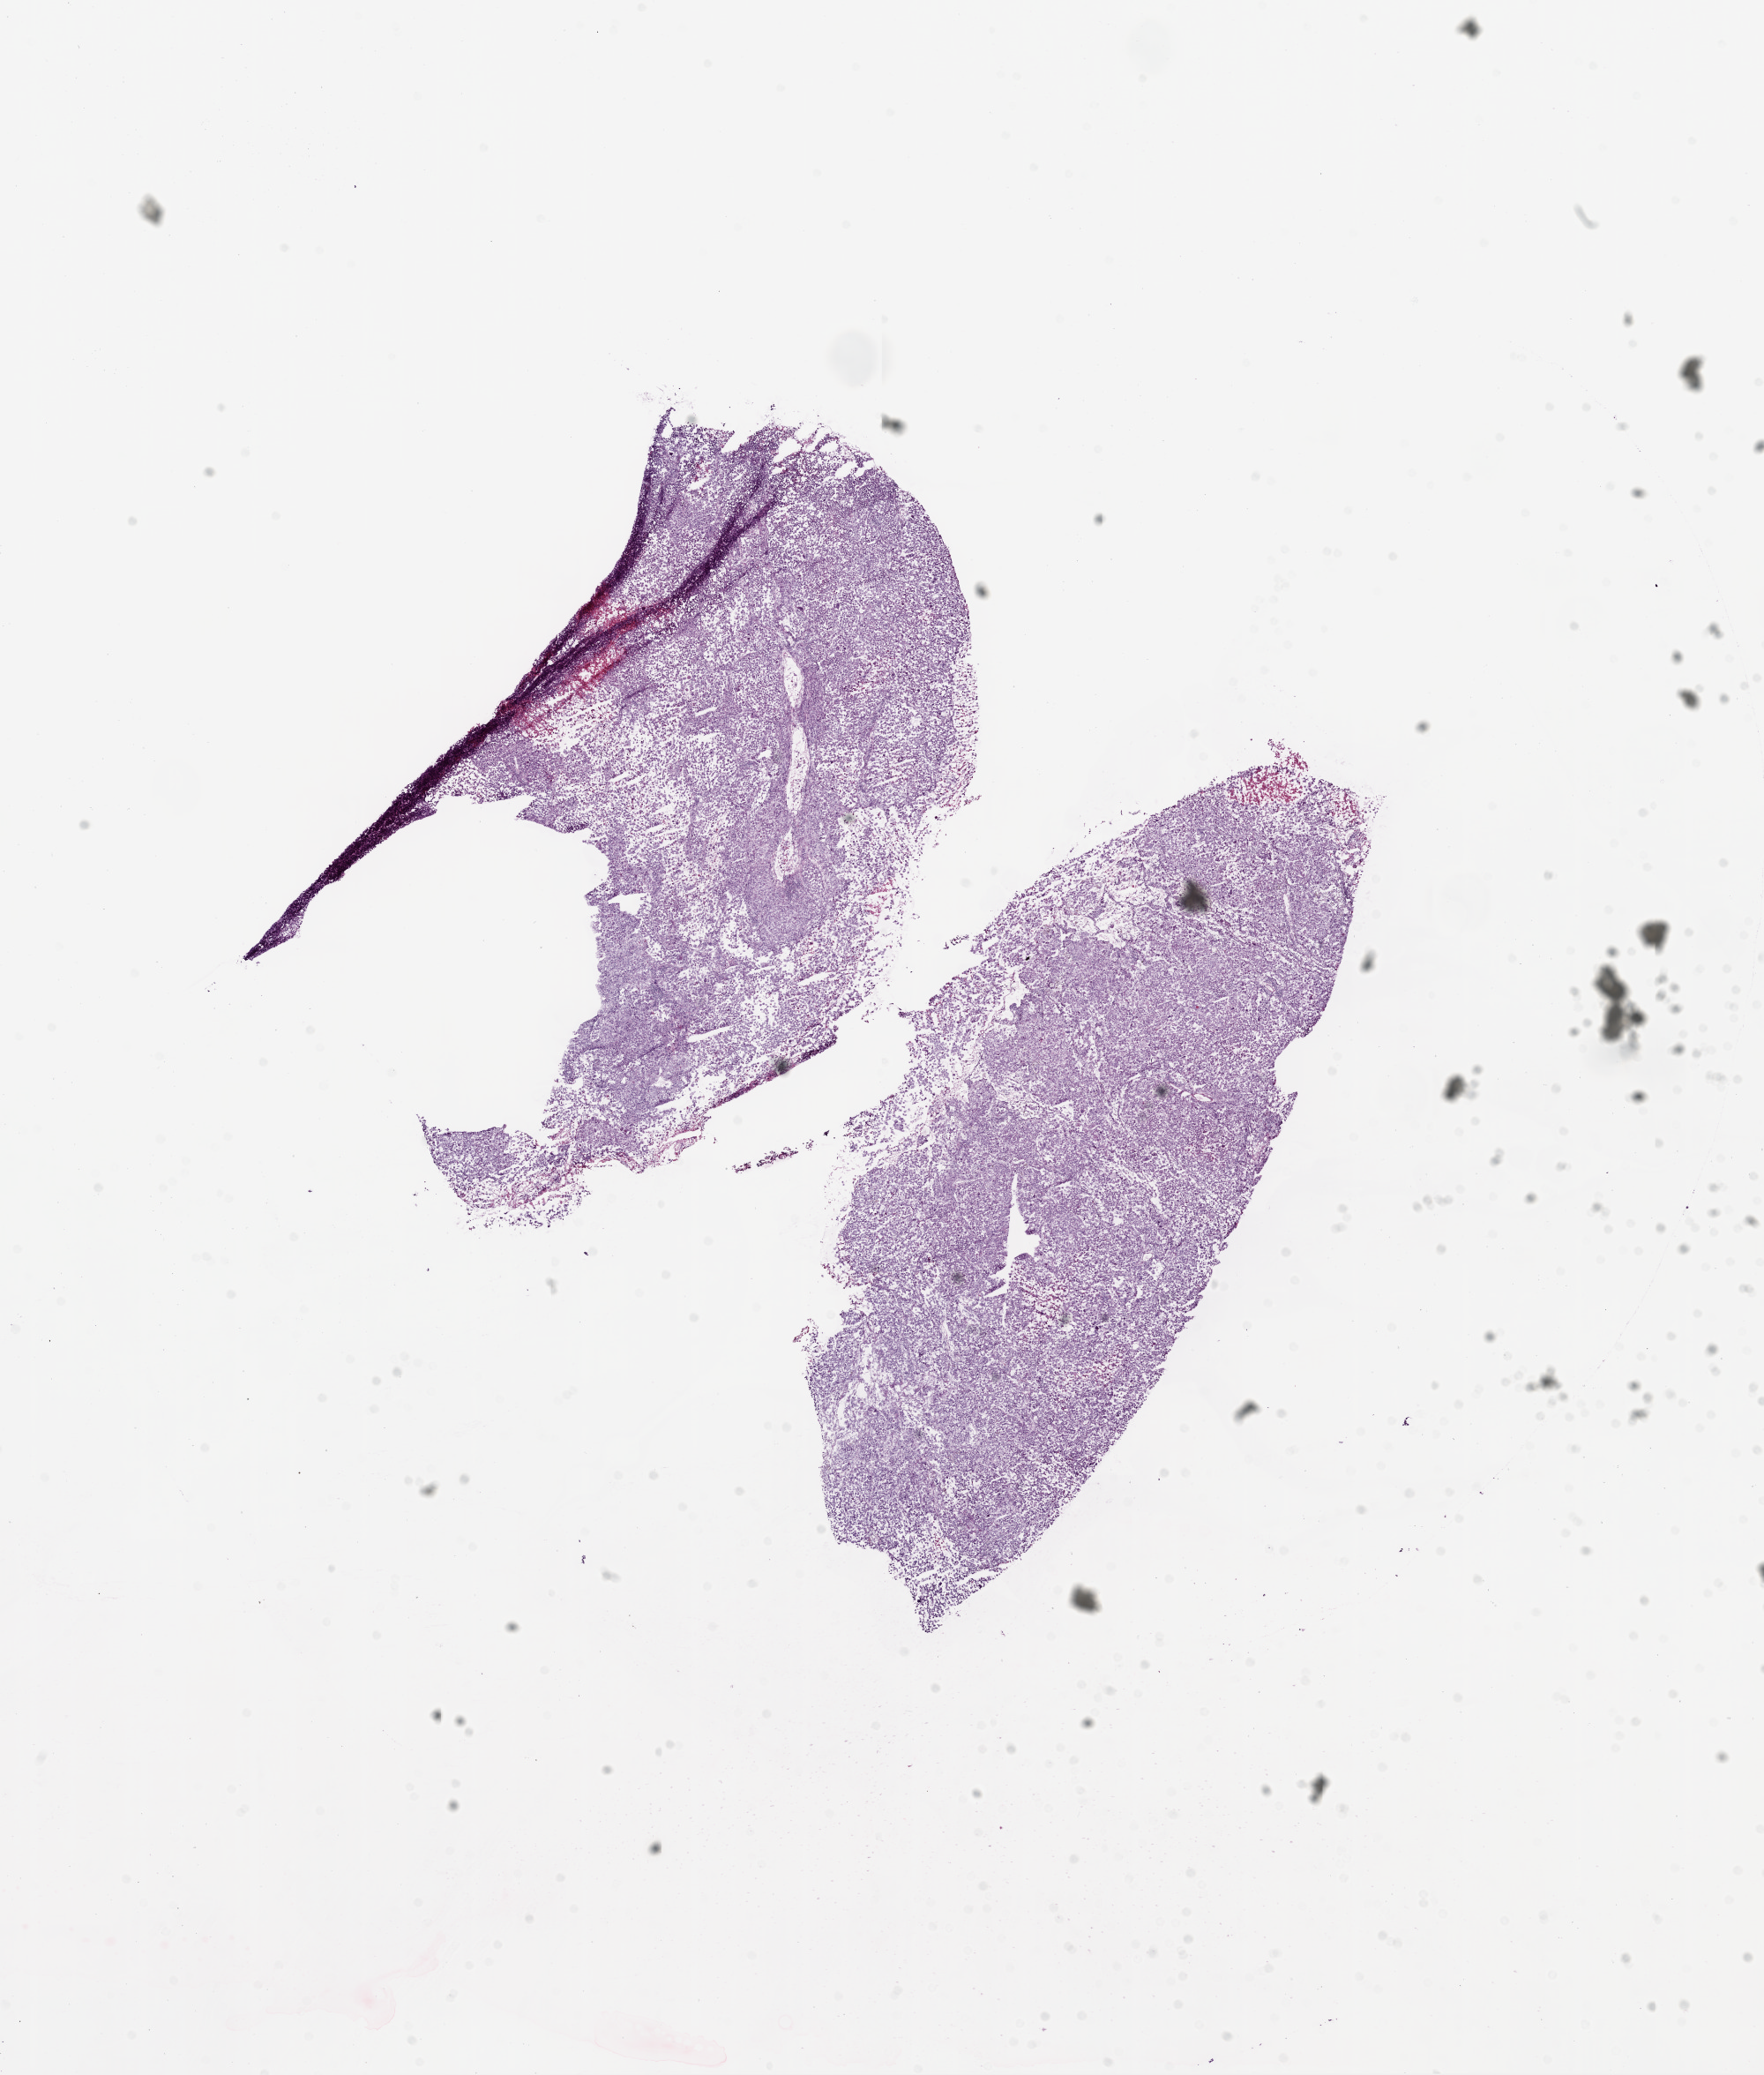
Whole-slide histology image, Hematoxylin and eosin (H&E) stained, whole scanned area (about 16.0 x 18.9 mm, from a 20x scan) shown as a low-resolution overview. Frozen section from the bottom of the tissue portion. Sample: primary tumour, lung. Male patient; age at initial diagnosis 57 years. Composition of this section per pathologist review: tumour cells 90%, tumour nuclei 80%.
Diagnosis: Adenocarcinoma with mixed subtypes (lower lobe, lung).